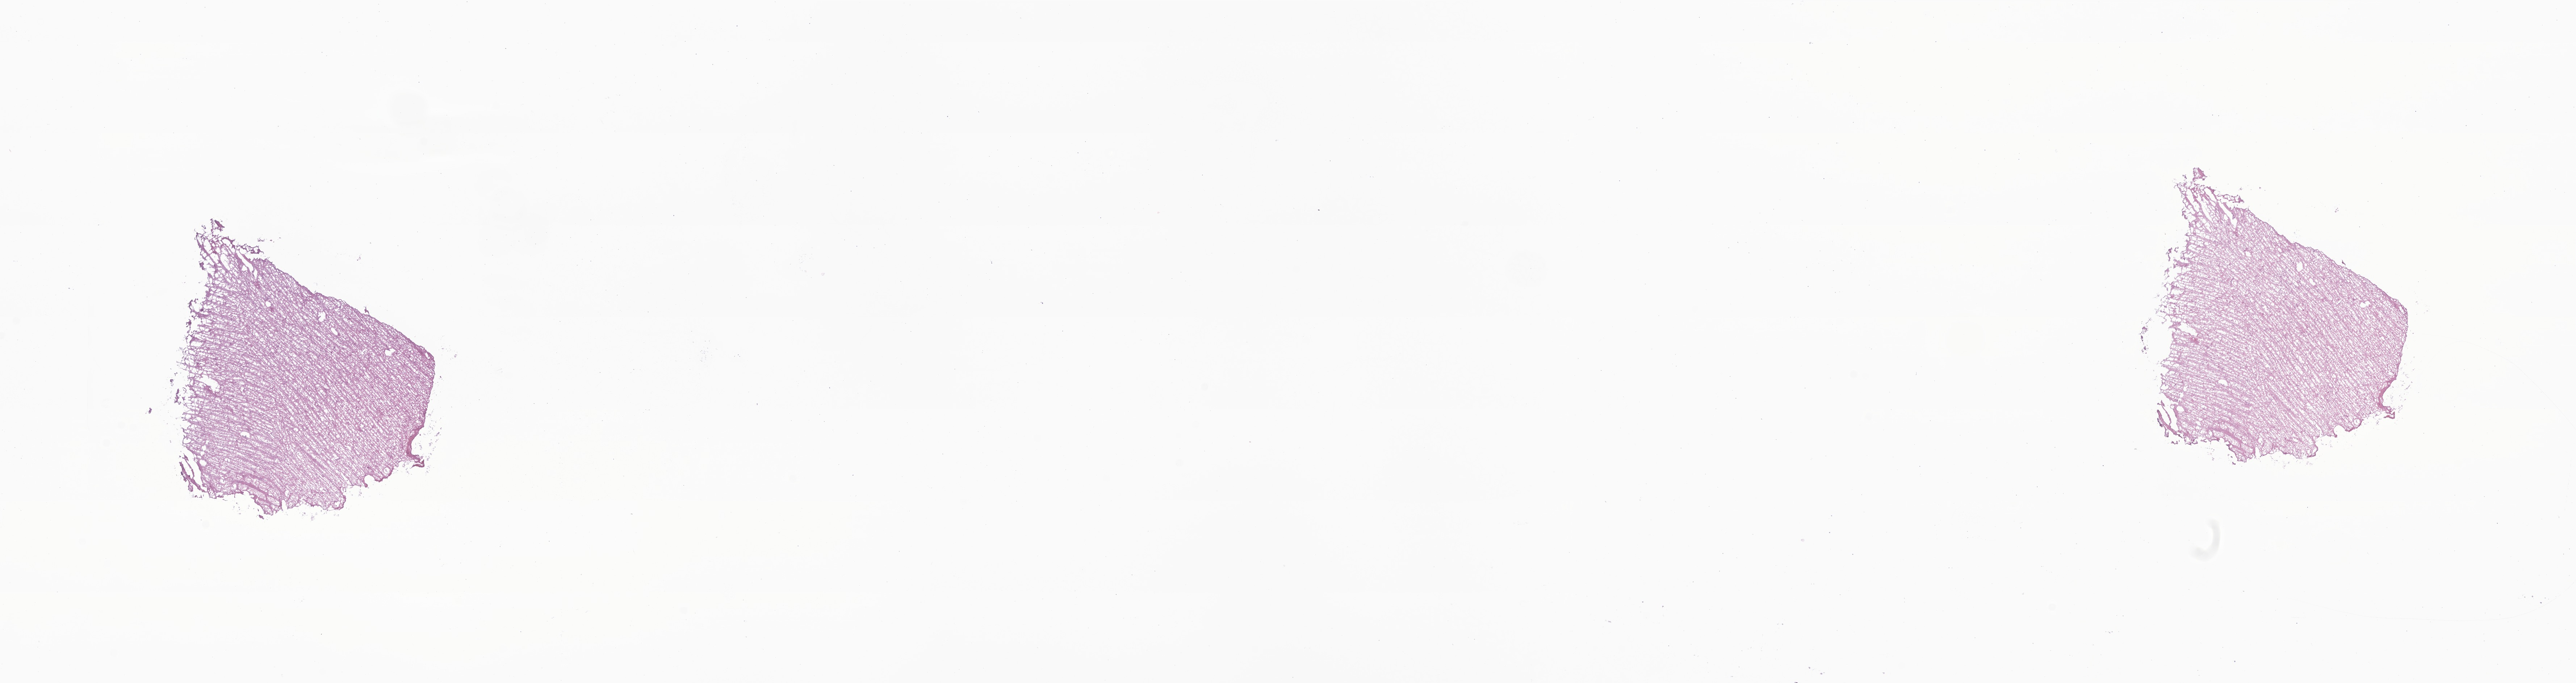
Whole-slide image, haematoxylin and eosin stain of tumor tissue from the brain, whole scanned area (about 30.0 x 7.9 mm) shown as a low-resolution overview; cryosection (OCT / tissue freezing medium). Patient female; age 210 months (17 years 6 months).
Recorded diagnosis: Glioma, malignant.